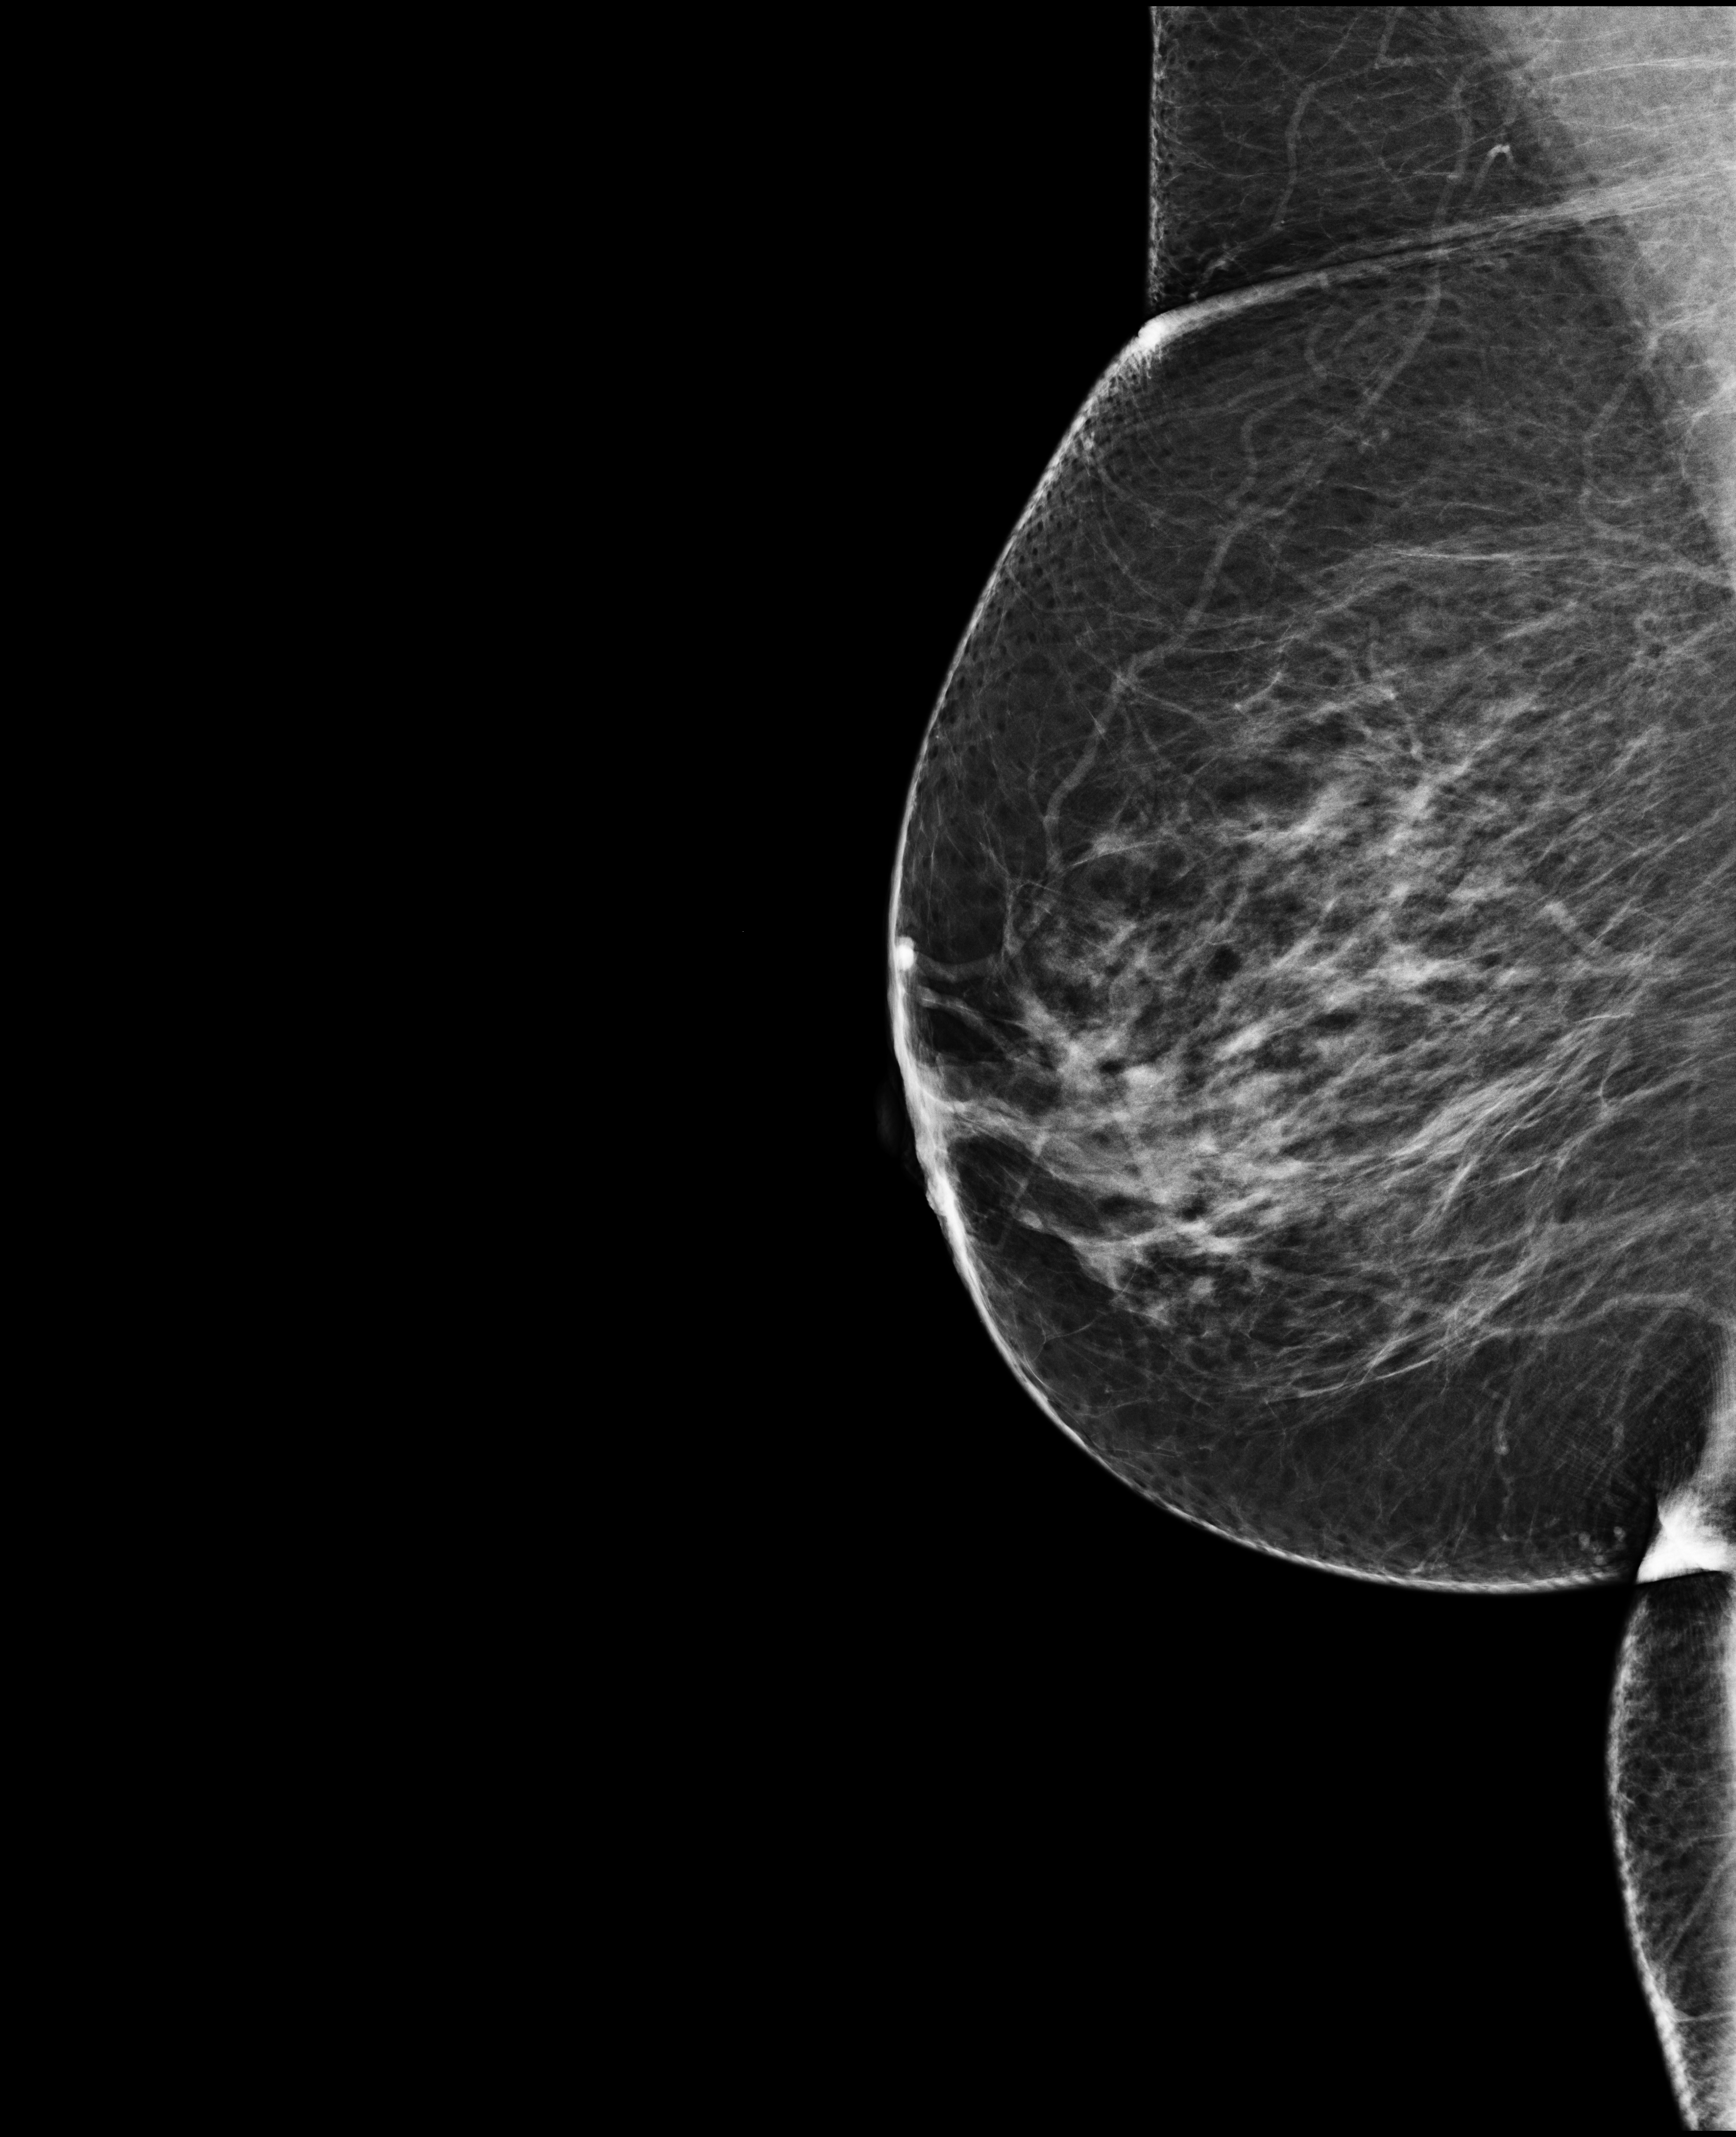
Digital mammogram (FFDM); right breast; mediolateral oblique (MLO) view; screening examination; compressed breast thickness 69 mm; system: Selenia Dimensions. Patient: female, 71 years.
Breast density at the screening exam (both breasts): heterogeneously dense (BI-RADS density category c). Final BI-RADS category for the screening round (tomosynthesis exam, both breasts): category 2. Recall: no recall after this screen.